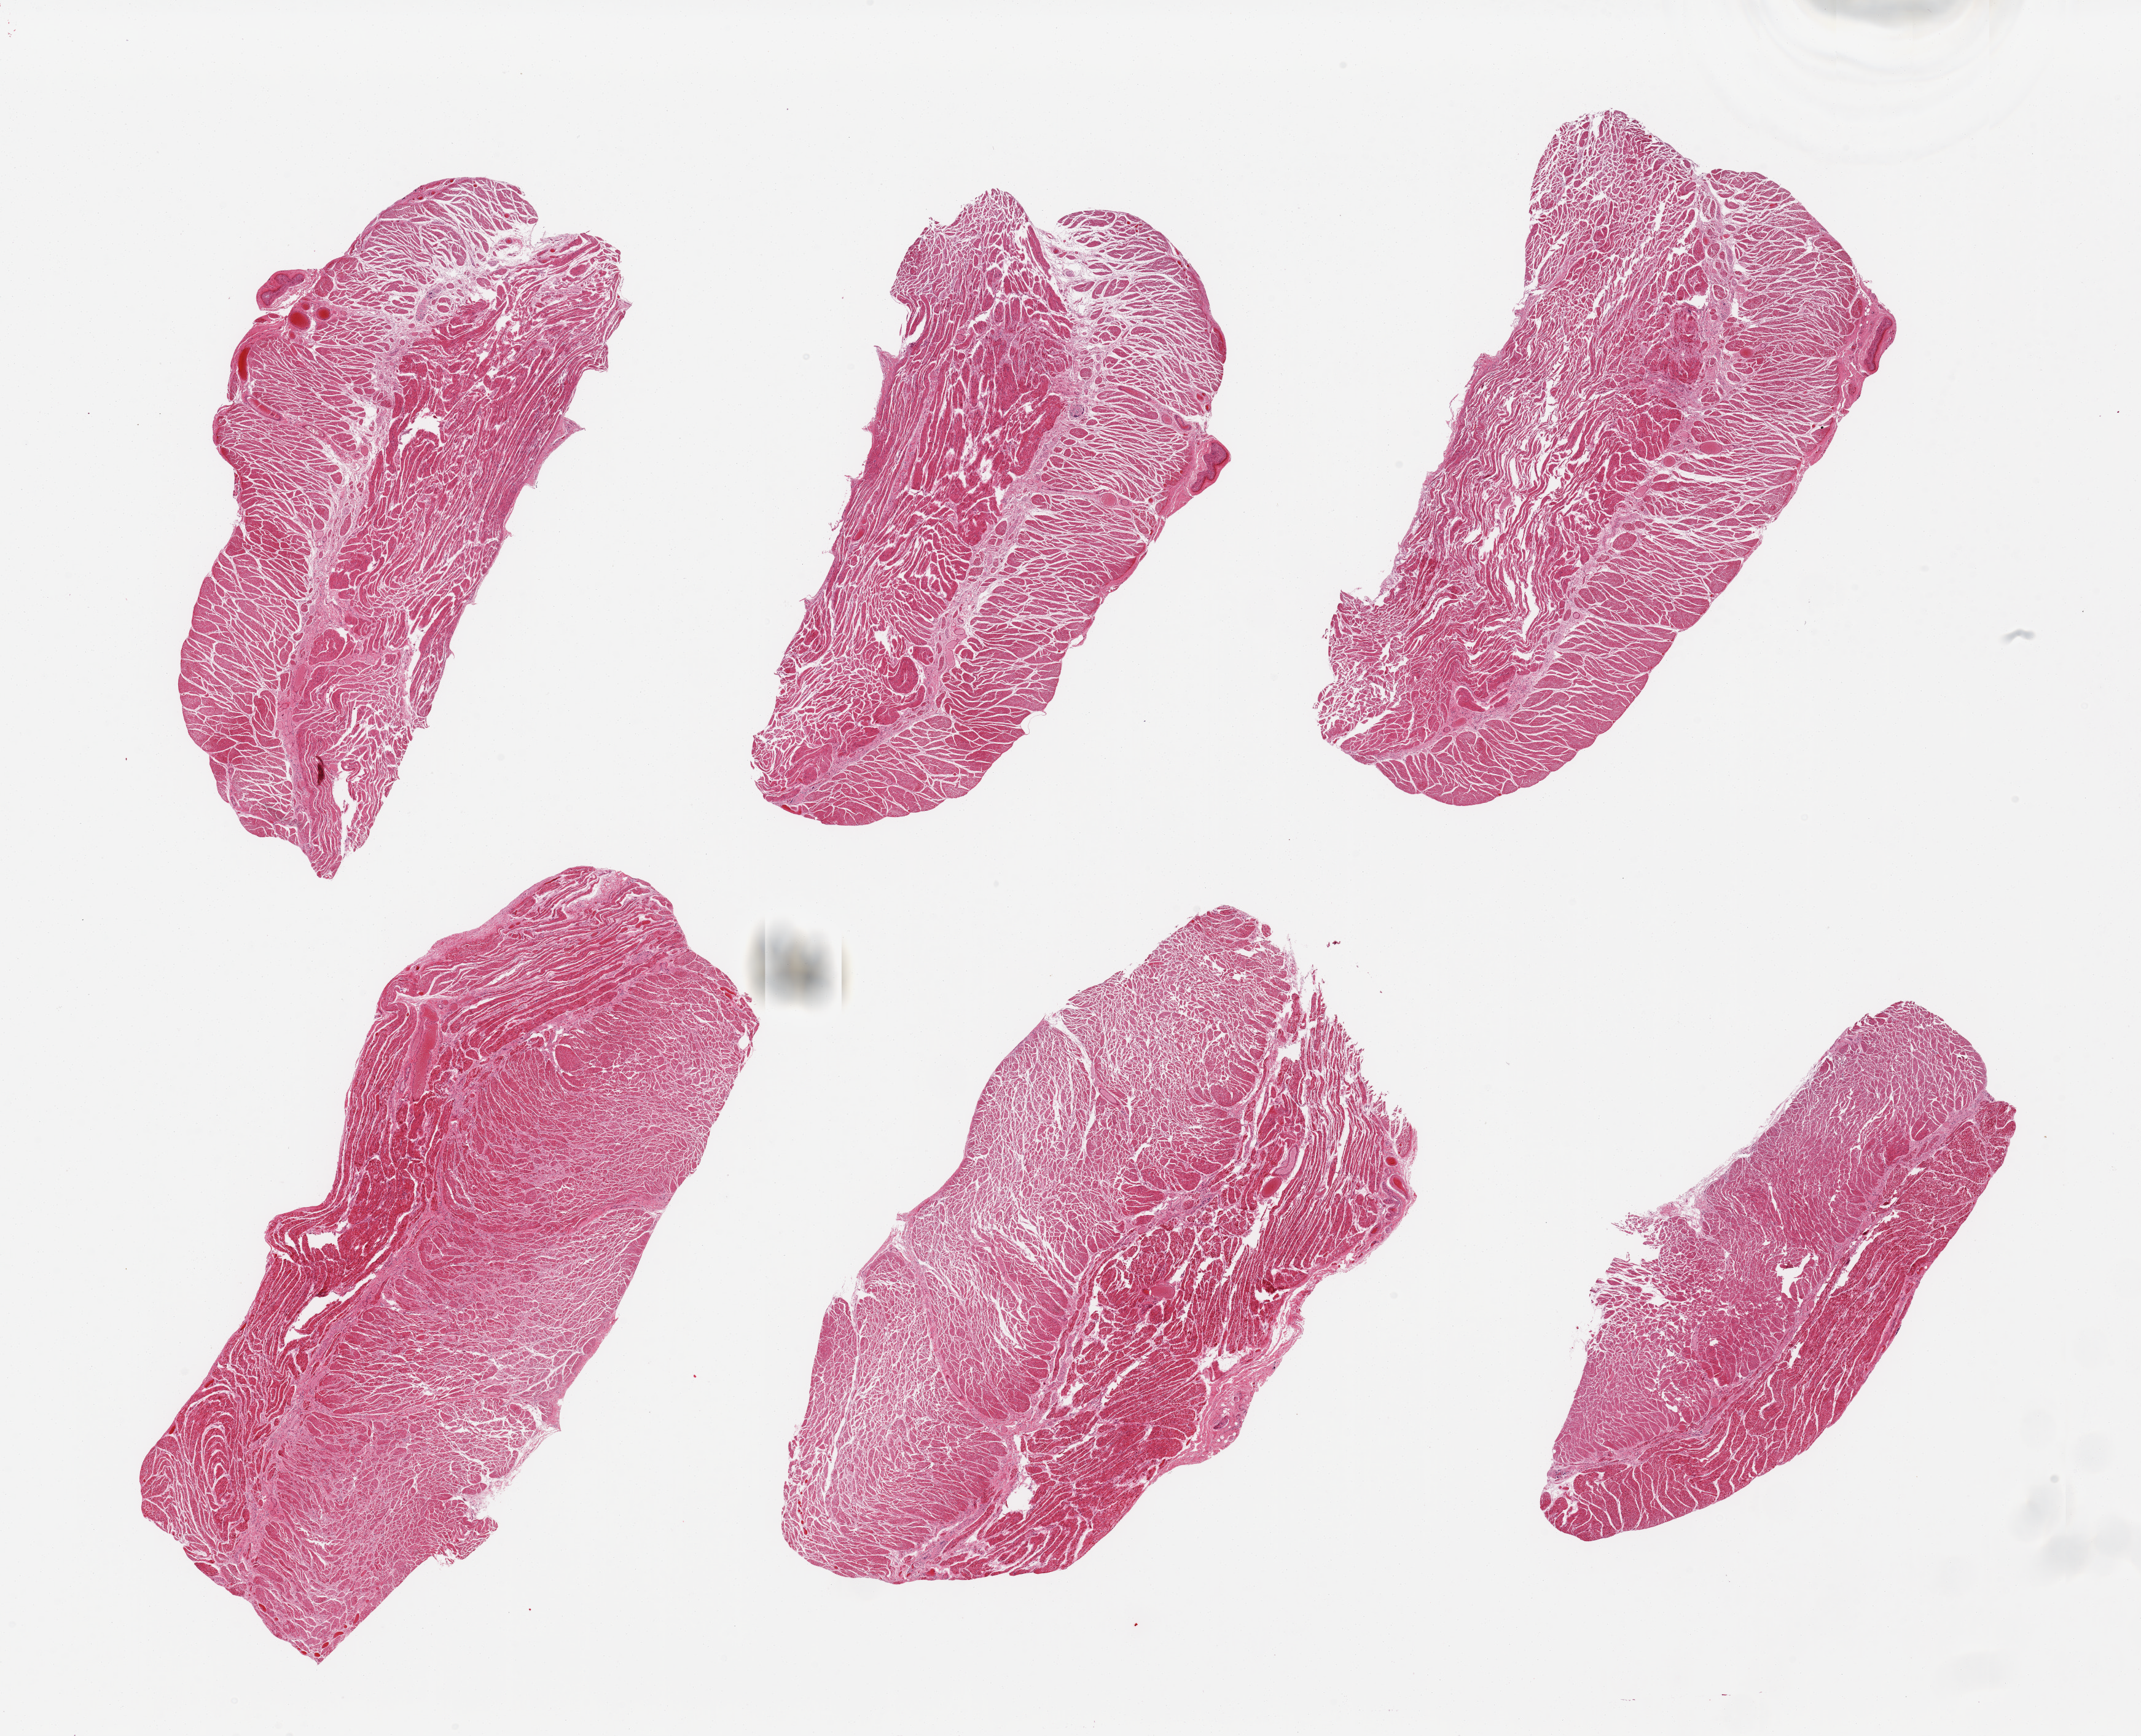
H&E whole-slide image — shown as a low-resolution overview of the whole scanned area (about 27.6 x 22.4 mm, slide scanned at 20x). PAXgene-fixed paraffin-embedded (PFPE) section. Section of esophageal muscle (target tissue). Donor tissue sample. Male donor.
Review note (as recorded): 6 pieces; well dissected muscularis.